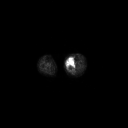
FDG PET of an extremity soft-tissue mass (from a PET/CT study), one axial slice. Position 136 of 223 along the scan axis. 3.27 mm slice thickness. 128 × 128 image matrix, field of view 700 × 700 mm. Patient: female, 70 years. From the clinical record (not read from this slice): histological type: extraskeletal high grade osteogenic sarcoma; grade: high; site of the primary tumour: left calf.
Structures marked on this image (expert contour drawn on MRI and transferred to this co-registered scan by the dataset authors):
- gross tumour volume (mass): bounding box [x1, y1, x2, y2] px = [66, 59, 74, 70]